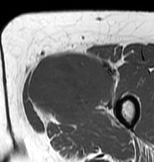
MRI of an extremity soft-tissue mass, one axial slice. MR volume resampled by the dataset authors to the PET/CT grid (not the native acquisition matrix). 3.27 mm slice thickness. 154 × 162 image matrix. Female patient. From the clinical record (not read from this slice): histological type: myxofibrosarcoma; grade: intermediate; site of the primary tumour: left thigh.
Annotated regions visible in this slice (expert contour drawn on MRI and transferred to this co-registered scan by the dataset authors):
- gross tumour volume including surrounding oedema: bounding box (x1, y1, x2, y2) in pixels: (26, 50, 118, 124)
- gross tumour volume (mass): (28, 54, 114, 119)